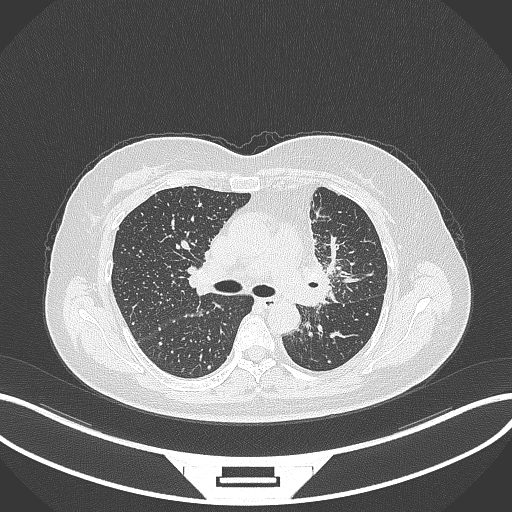
Chest CT, one axial slice; slice 208 of 348 in the series (ordered by position); 120 kVp; lung window (W 1500 / L -600 HU); 1 mm slice thickness; 512 × 512 image matrix, field of view 400 × 400 mm. Female patient, age 49 years. Case-level facts recorded for this patient, not image findings: clinical TNM (as recorded): T1c N0 M1.
Structures marked on this image (rectangle marked by the reading radiologist):
- lung tumour (recorded histology: adenocarcinoma): bounding box (x1, y1, x2, y2) in pixels: (294, 250, 337, 308)